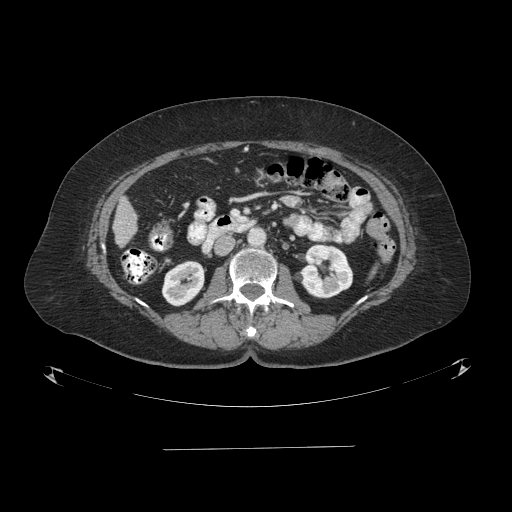
Contrast-enhanced abdominal CT (liver protocol), one axial slice; slice 20 of 103 in the series (ordered by position); reconstruction kernel STANDARD; 120 kVp; one of 2 acquisitions stored at this slice position; soft-tissue window (W 400 / L 40 HU); 2.5 mm slice thickness; 512 × 512 image matrix. From the clinical record (not read from this slice): diagnosis: hepatocellular carcinoma (patient treated with transarterial chemoembolisation; whether this scan precedes or follows treatment is not stated here); TNM stage (as recorded): Stage-IIIA; Child-Pugh class: A; tumour differentiation: poorly differentiated; tumour nodularity: multinodular.
Annotated regions visible in this slice (semi-automatic segmentation, software-assisted and operator-edited):
- liver parenchyma outside the tumour (the mass and vessels are separate outlines, so this box may not span the whole liver): bounding box [x1, y1, x2, y2] px = [112, 196, 136, 247]